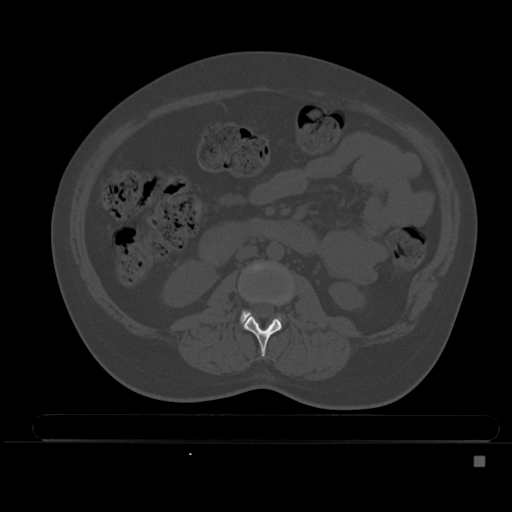
CT including the spine, one axial slice. Slice 164 of 495 in the series (ordered by position). Bone window (W 1800 / L 400 HU). 1.5 mm slice thickness. 512 × 512 image matrix, field of view 404 × 404 mm. Patient: female, 33 years. From the clinical record (not read from this slice): primary cancer: breast.
Outlined on this slice (semi-automatically segmented with operator editing):
- L2 vertebra: bounding box (x1, y1, x2, y2) in pixels: (244, 286, 292, 357)
- L3 vertebra: (240, 265, 261, 323)